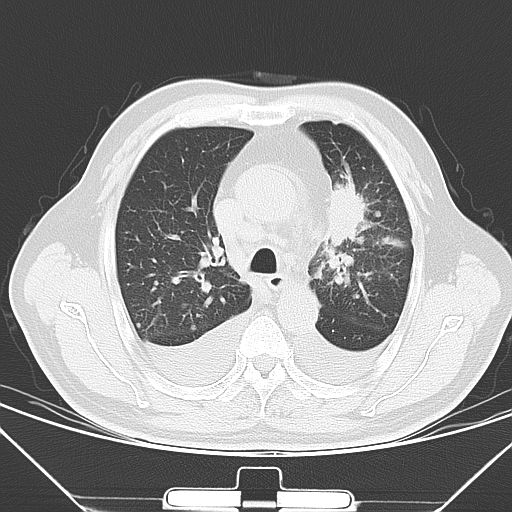
Chest CT, one axial slice; position 44 of 66 along the scan axis; lung window (W 1500 / L -600 HU); 512 × 512 image matrix. Male patient, age 66 years. Case-level facts recorded for this patient, not image findings: clinical TNM (as recorded): T1c N0 M0.
Outlined on this slice (rectangle marked by the reading radiologist):
- lung tumour (recorded histology: adenocarcinoma): bounding box [x1, y1, x2, y2] px = [324, 177, 369, 248]